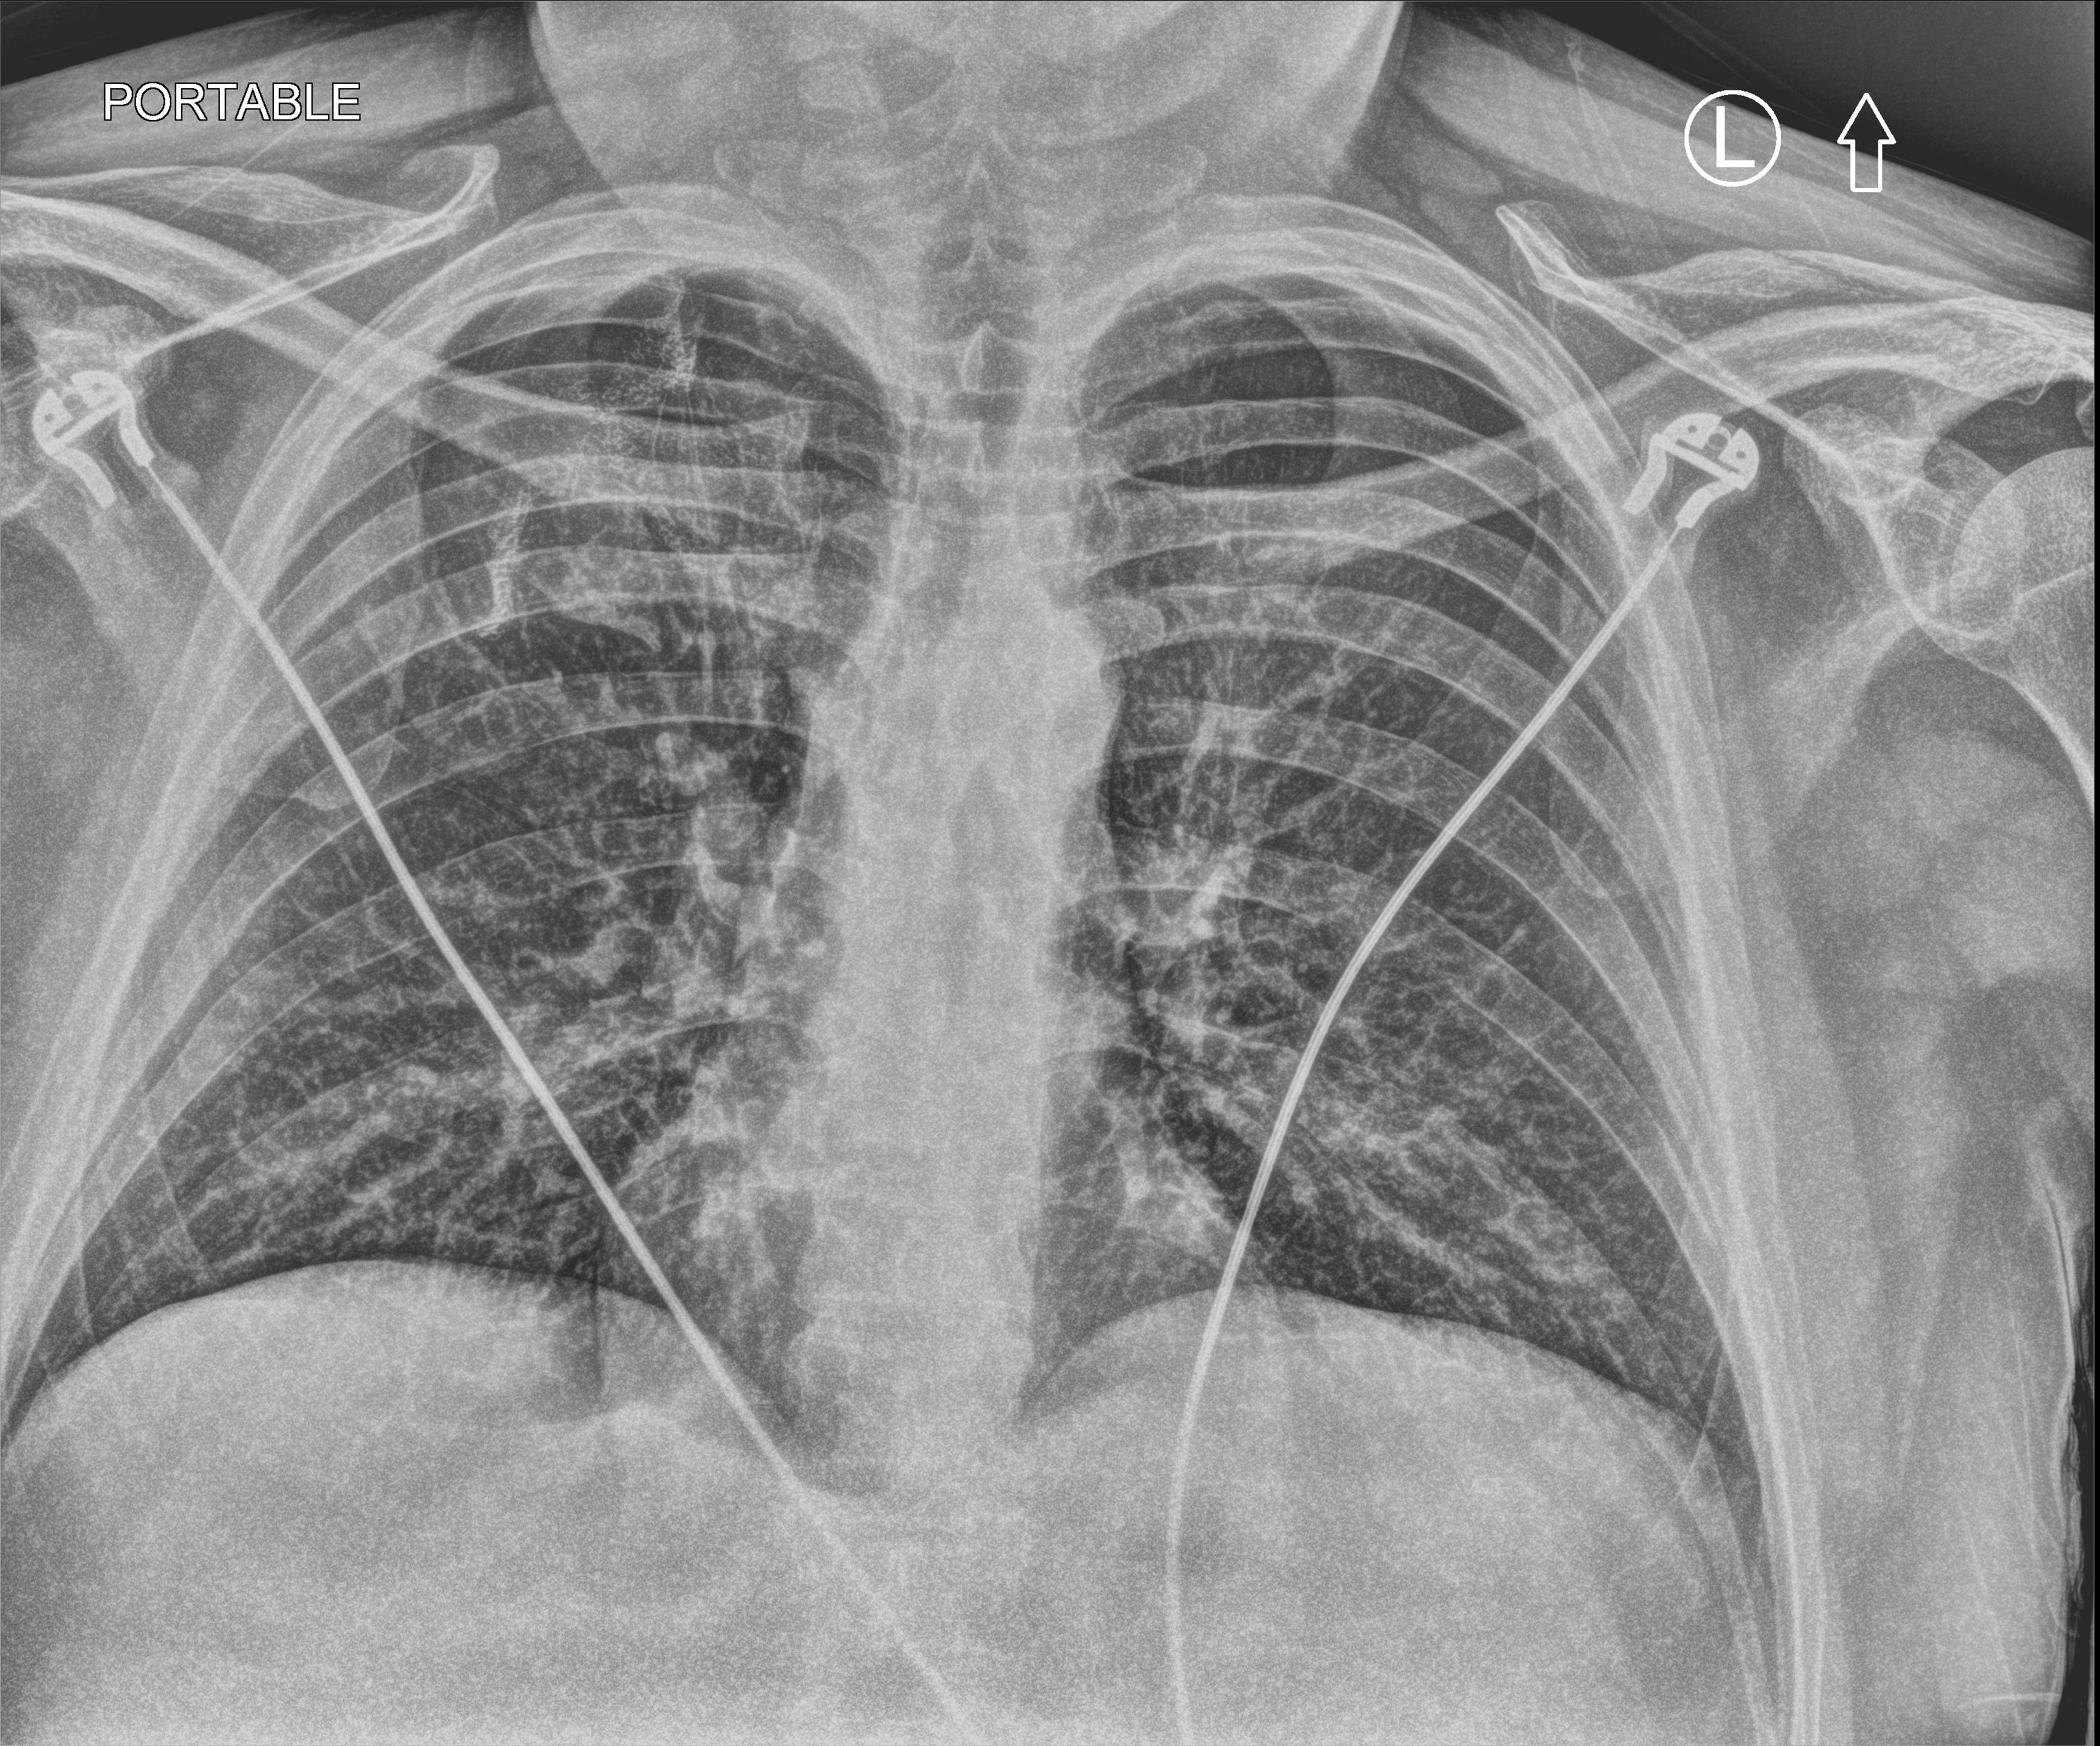
Bedside chest radiograph (computed radiography), anteroposterior (AP) projection. Male patient hospitalised with COVID-19, age 18–59 years.
Hospital-stay facts (about this admission, not read from this image; timing relative to this image not recorded): admitted to intensive care during this hospital stay: no.